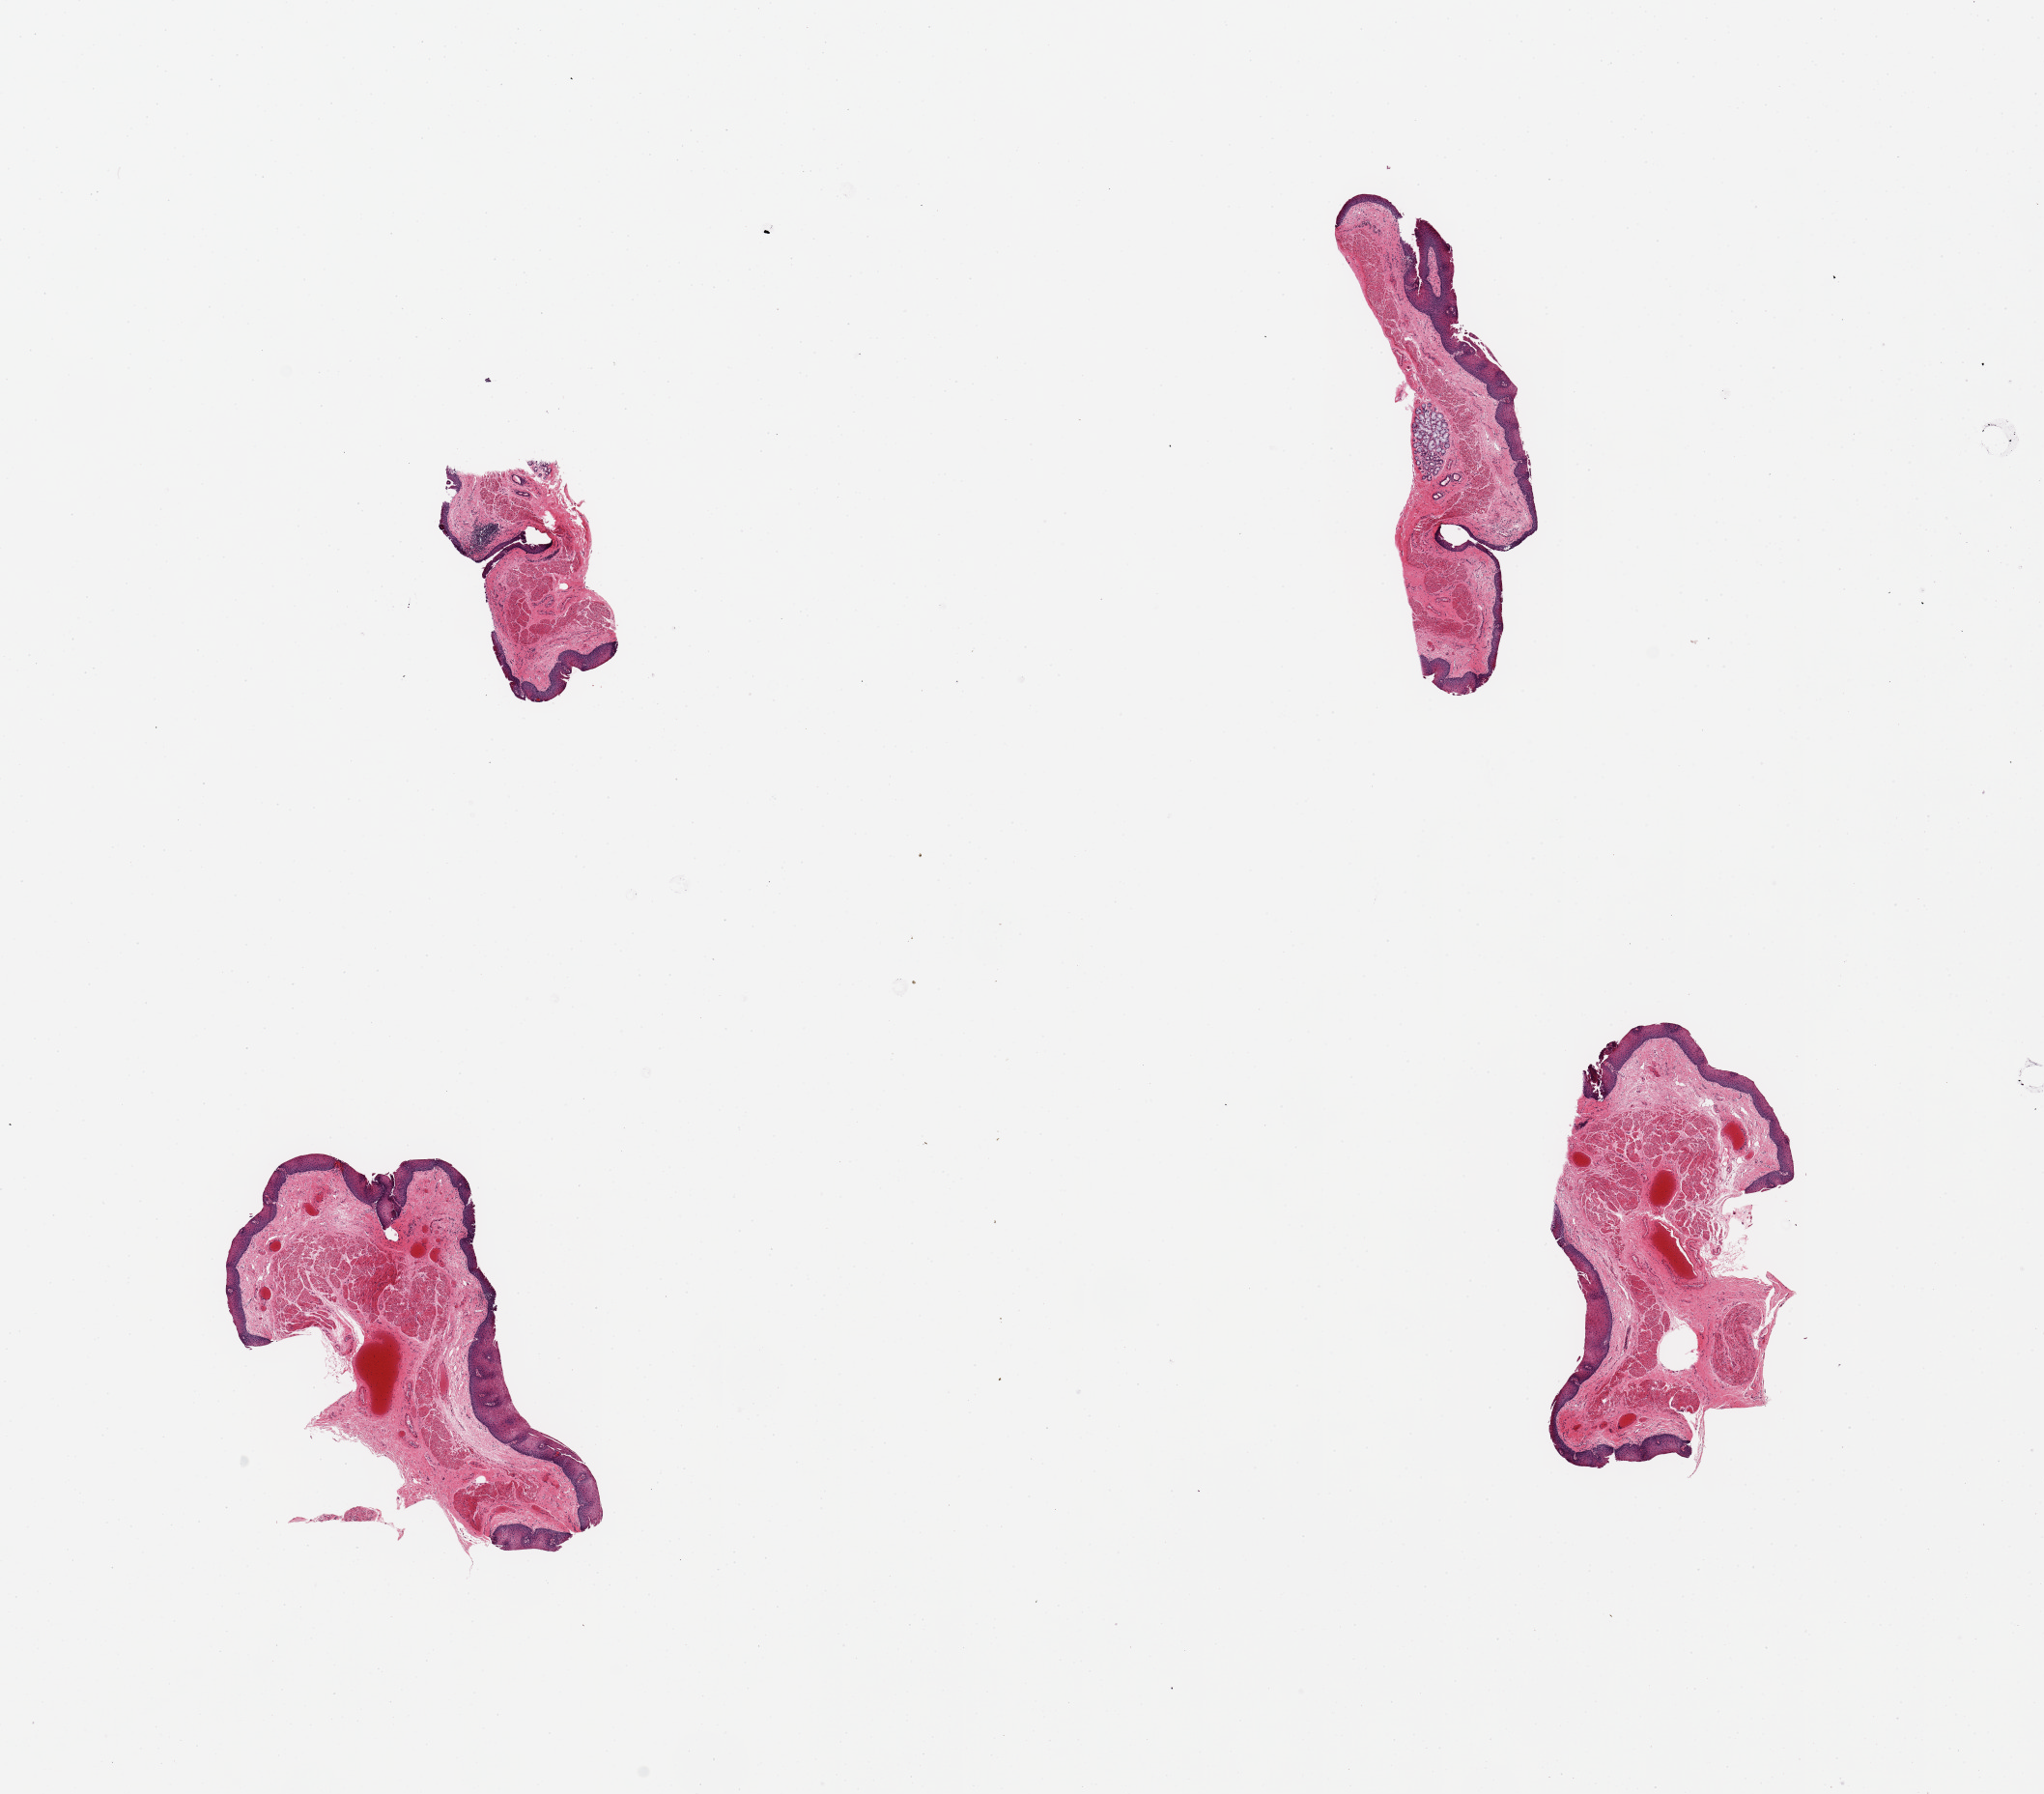
Haematoxylin and eosin whole-slide image, brightfield — a low-resolution overview of the entire scanned area, about 16.7 x 14.7 mm. PAXgene-fixed paraffin-embedded (PFPE) section. Section of esophageal mucous membrane (target tissue). Donor tissue sample. Donor: male.
Reviewer comment on this tissue sample: 4 pieces; moderate venous vascular congestiopn.